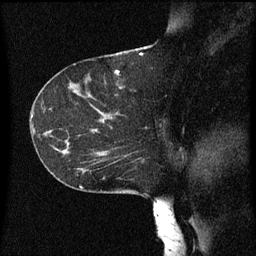
Breast MRI (dynamic contrast-enhanced), one sagittal slice; slice 34 of 60 in the series (ordered by position); dynamic contrast-enhanced series, image 2 of 3 at this slice position (ordered by acquisition); 1.5 T; TE 4.2 ms, TR 8 ms; 2 mm slice thickness; 256 × 256 image matrix, field of view 200 × 200 mm. Patient: female, 55 years.
Annotated regions visible in this slice (semi-automatically segmented with operator editing):
- analysis volume of interest (the breast-tissue region the enhancement analysis was run in; not a lesion): bounding box [x1, y1, x2, y2] px = [46, 124, 151, 183]
- tumour enhancement mask (voxels above the 70 % enhancement threshold inside the analysis volume of interest): [78, 128, 123, 177]